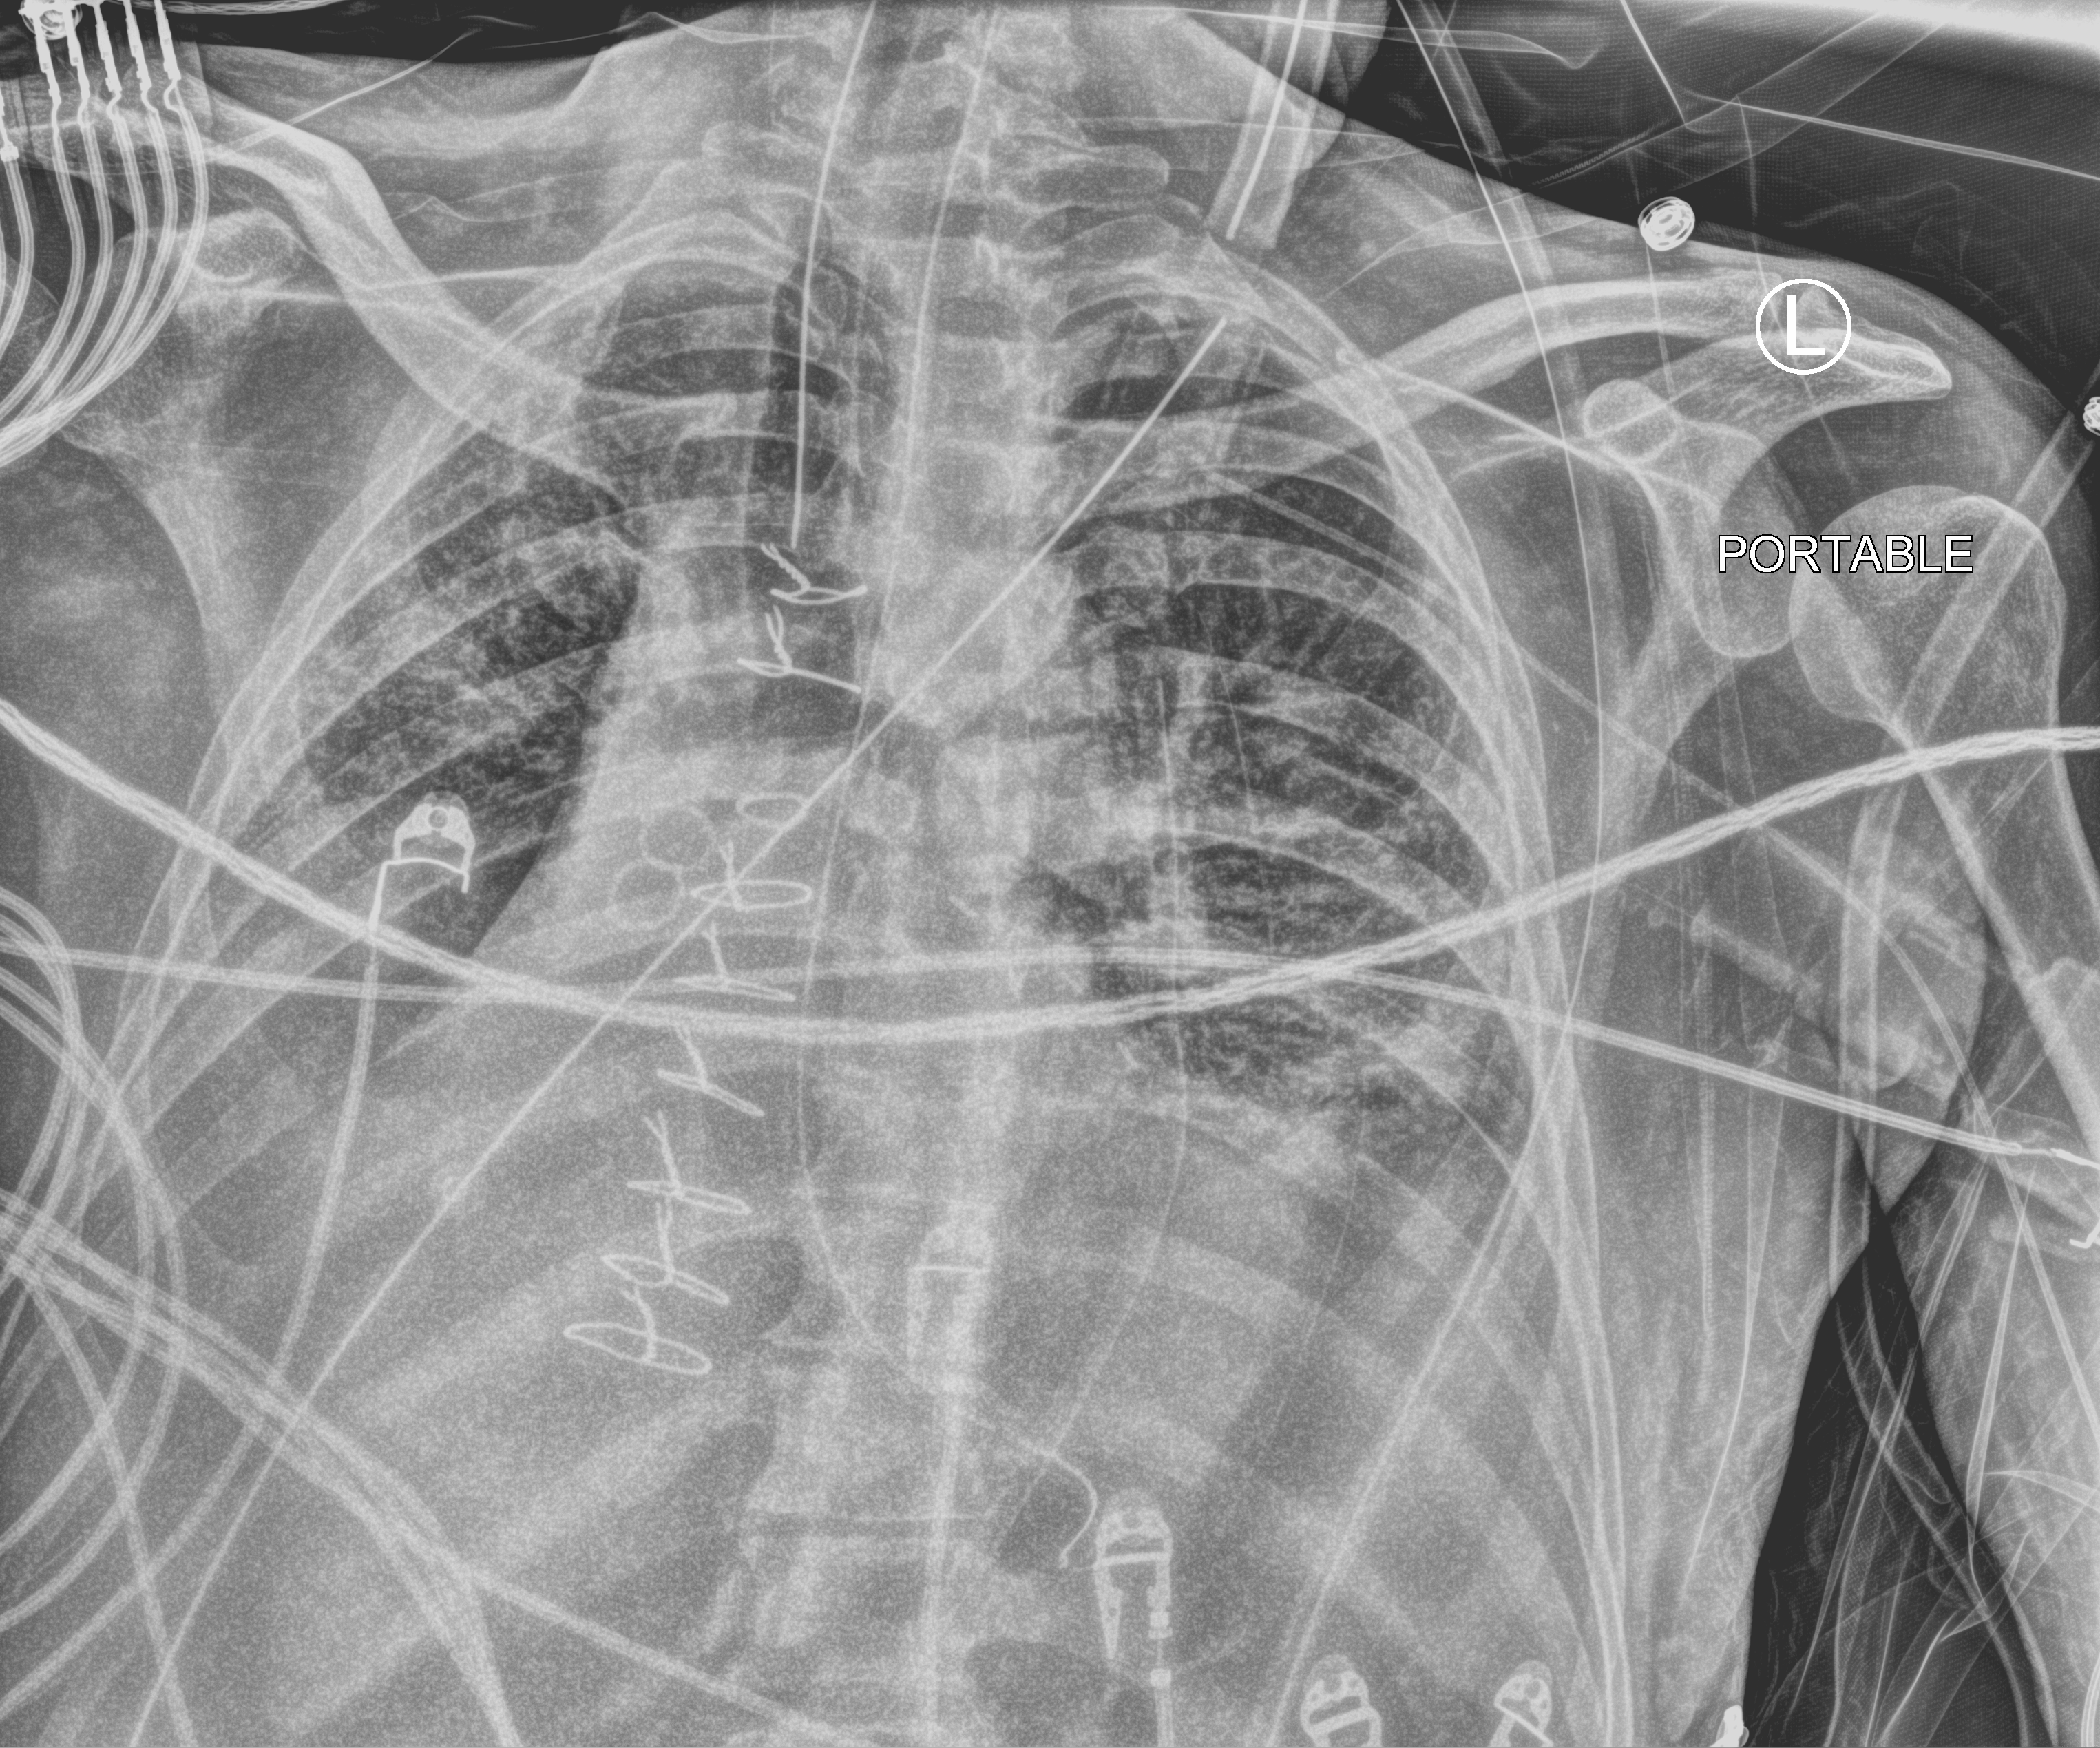
Bedside chest radiograph (computed radiography). Patient hospitalised with COVID-19; male, aged 18–59 years.
Hospital-stay facts (about this admission, not read from this image; timing relative to this image not recorded): admitted to intensive care during this hospital stay: yes; mechanically ventilated during this hospital stay: yes.